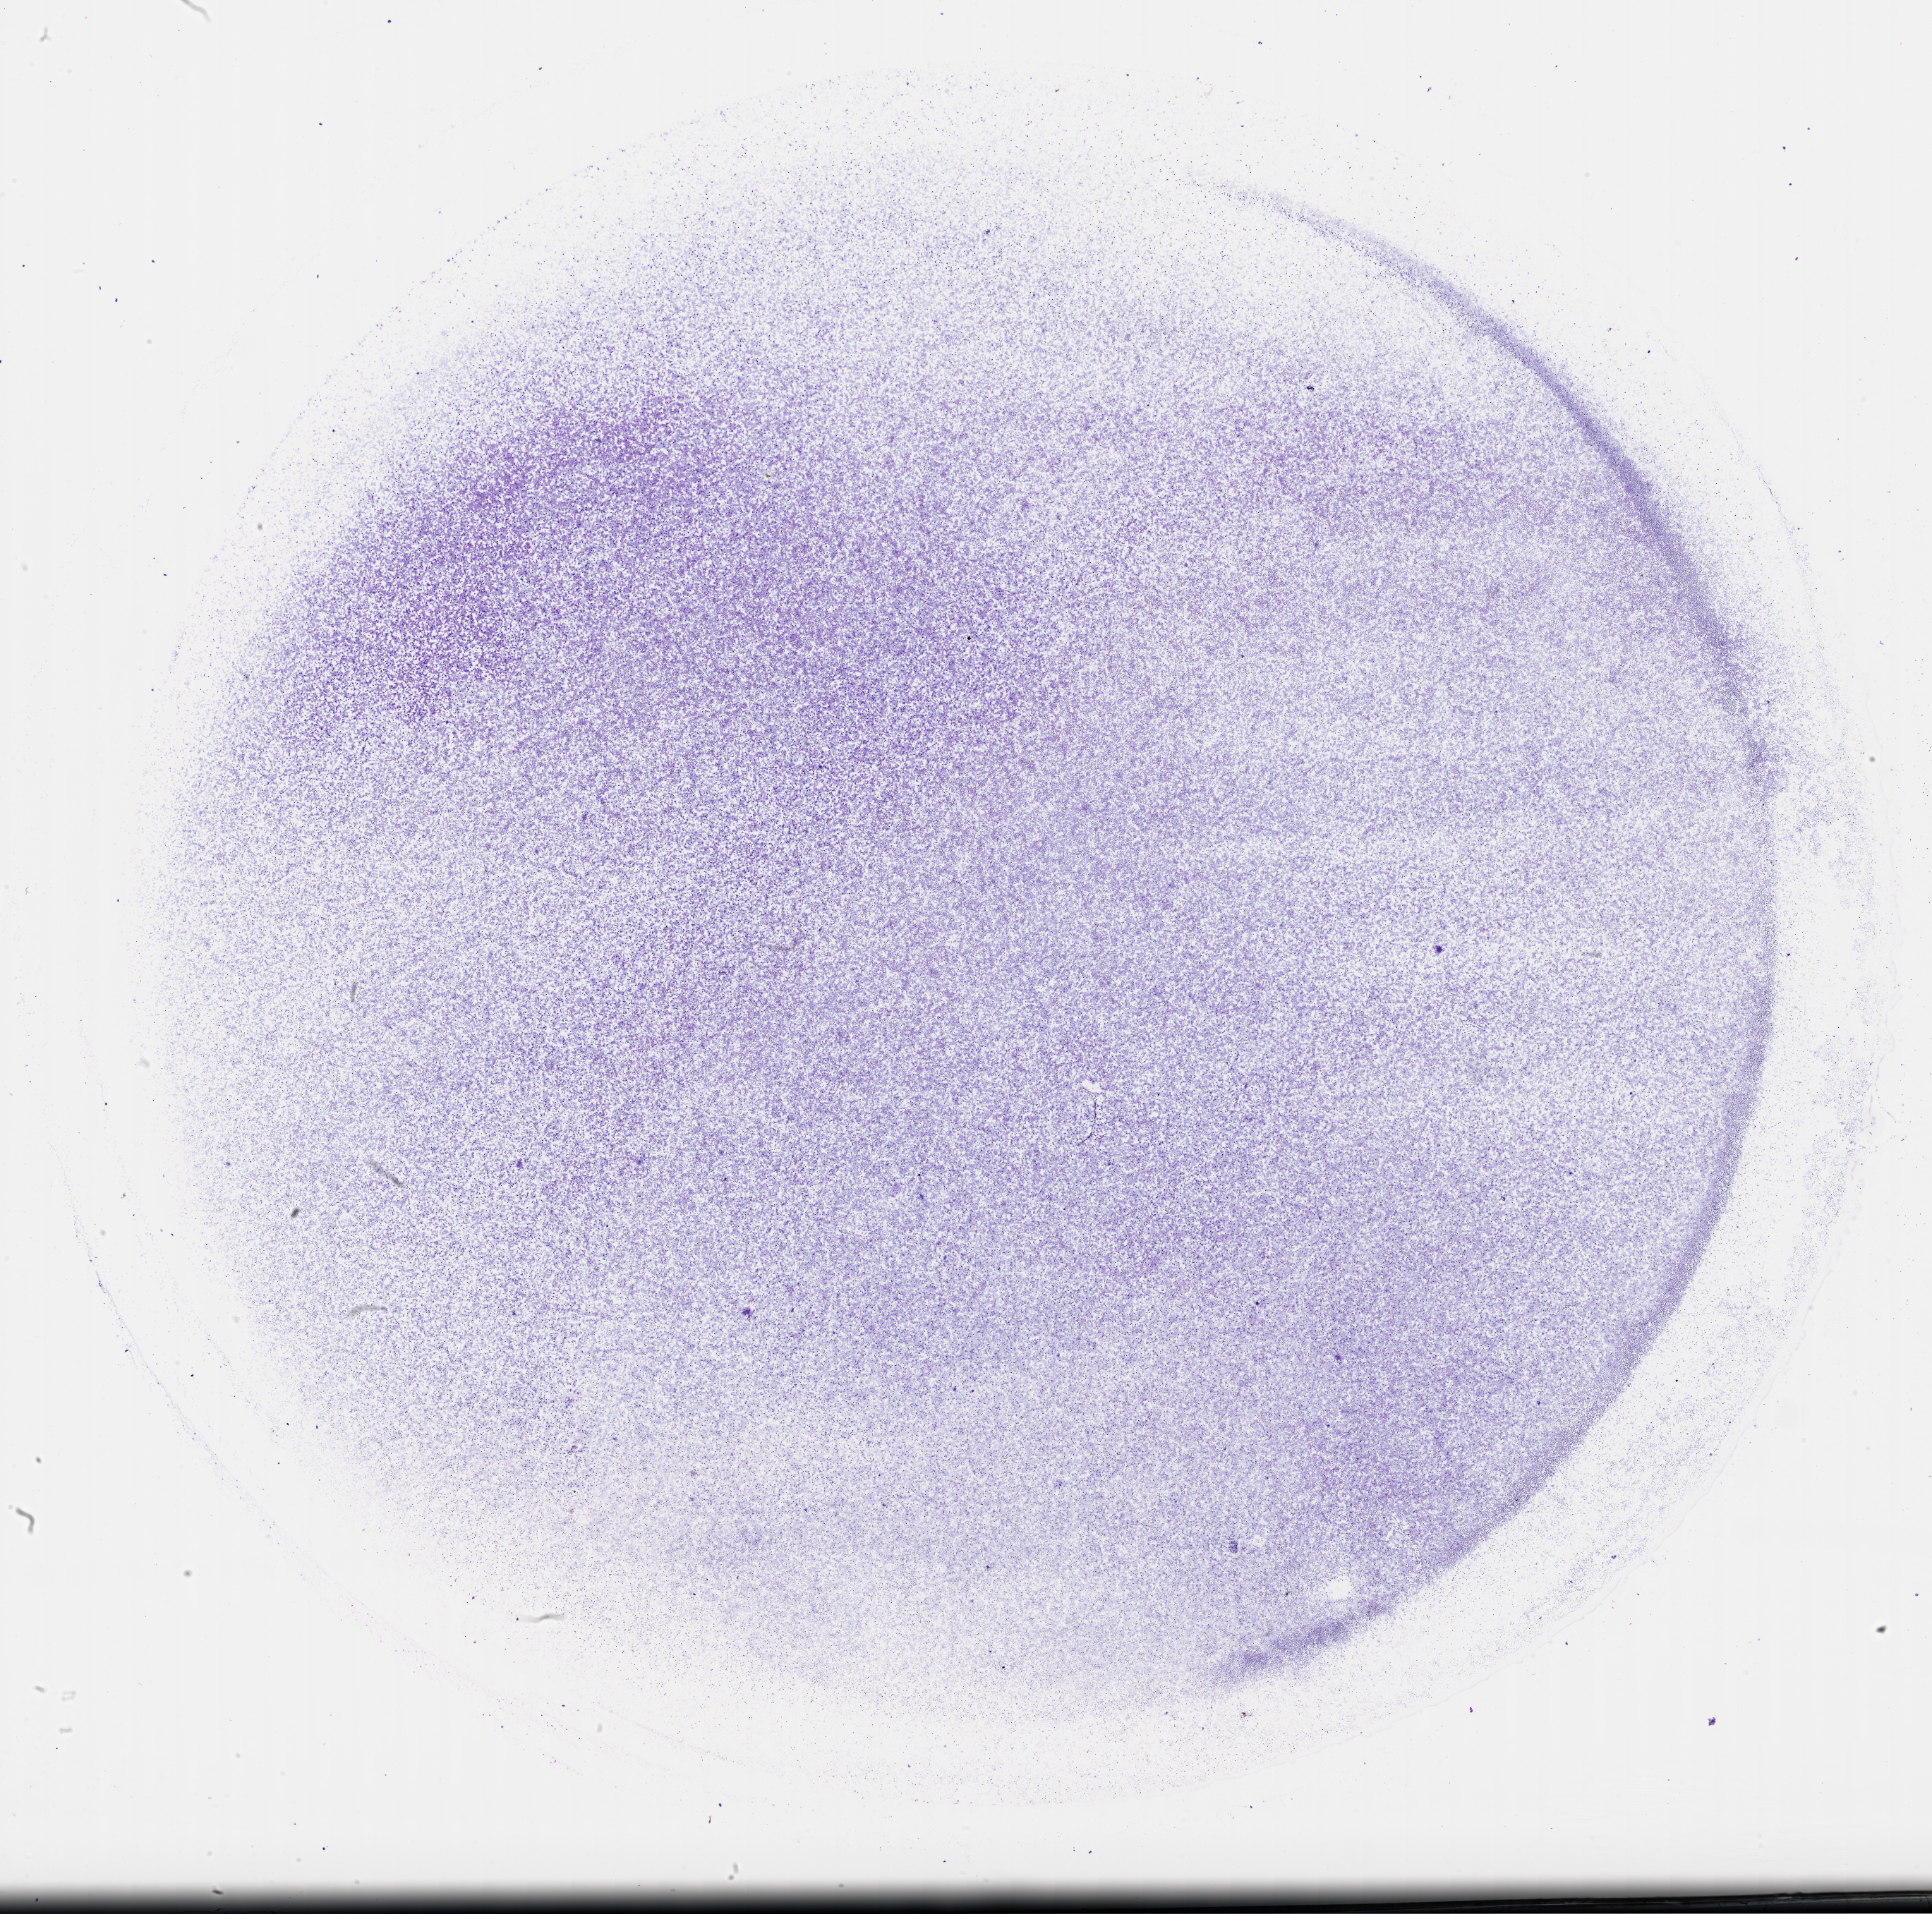
Hematoxylin and eosin (H&E) stained whole-slide image, low-resolution overview of the scanned area, about 22.1 x 21.9 mm (acquisition: 40x scan). Bone marrow (leukaemic) sample. 66-year-old male patient.
Diagnosis: Acute Myeloid Leukemia.